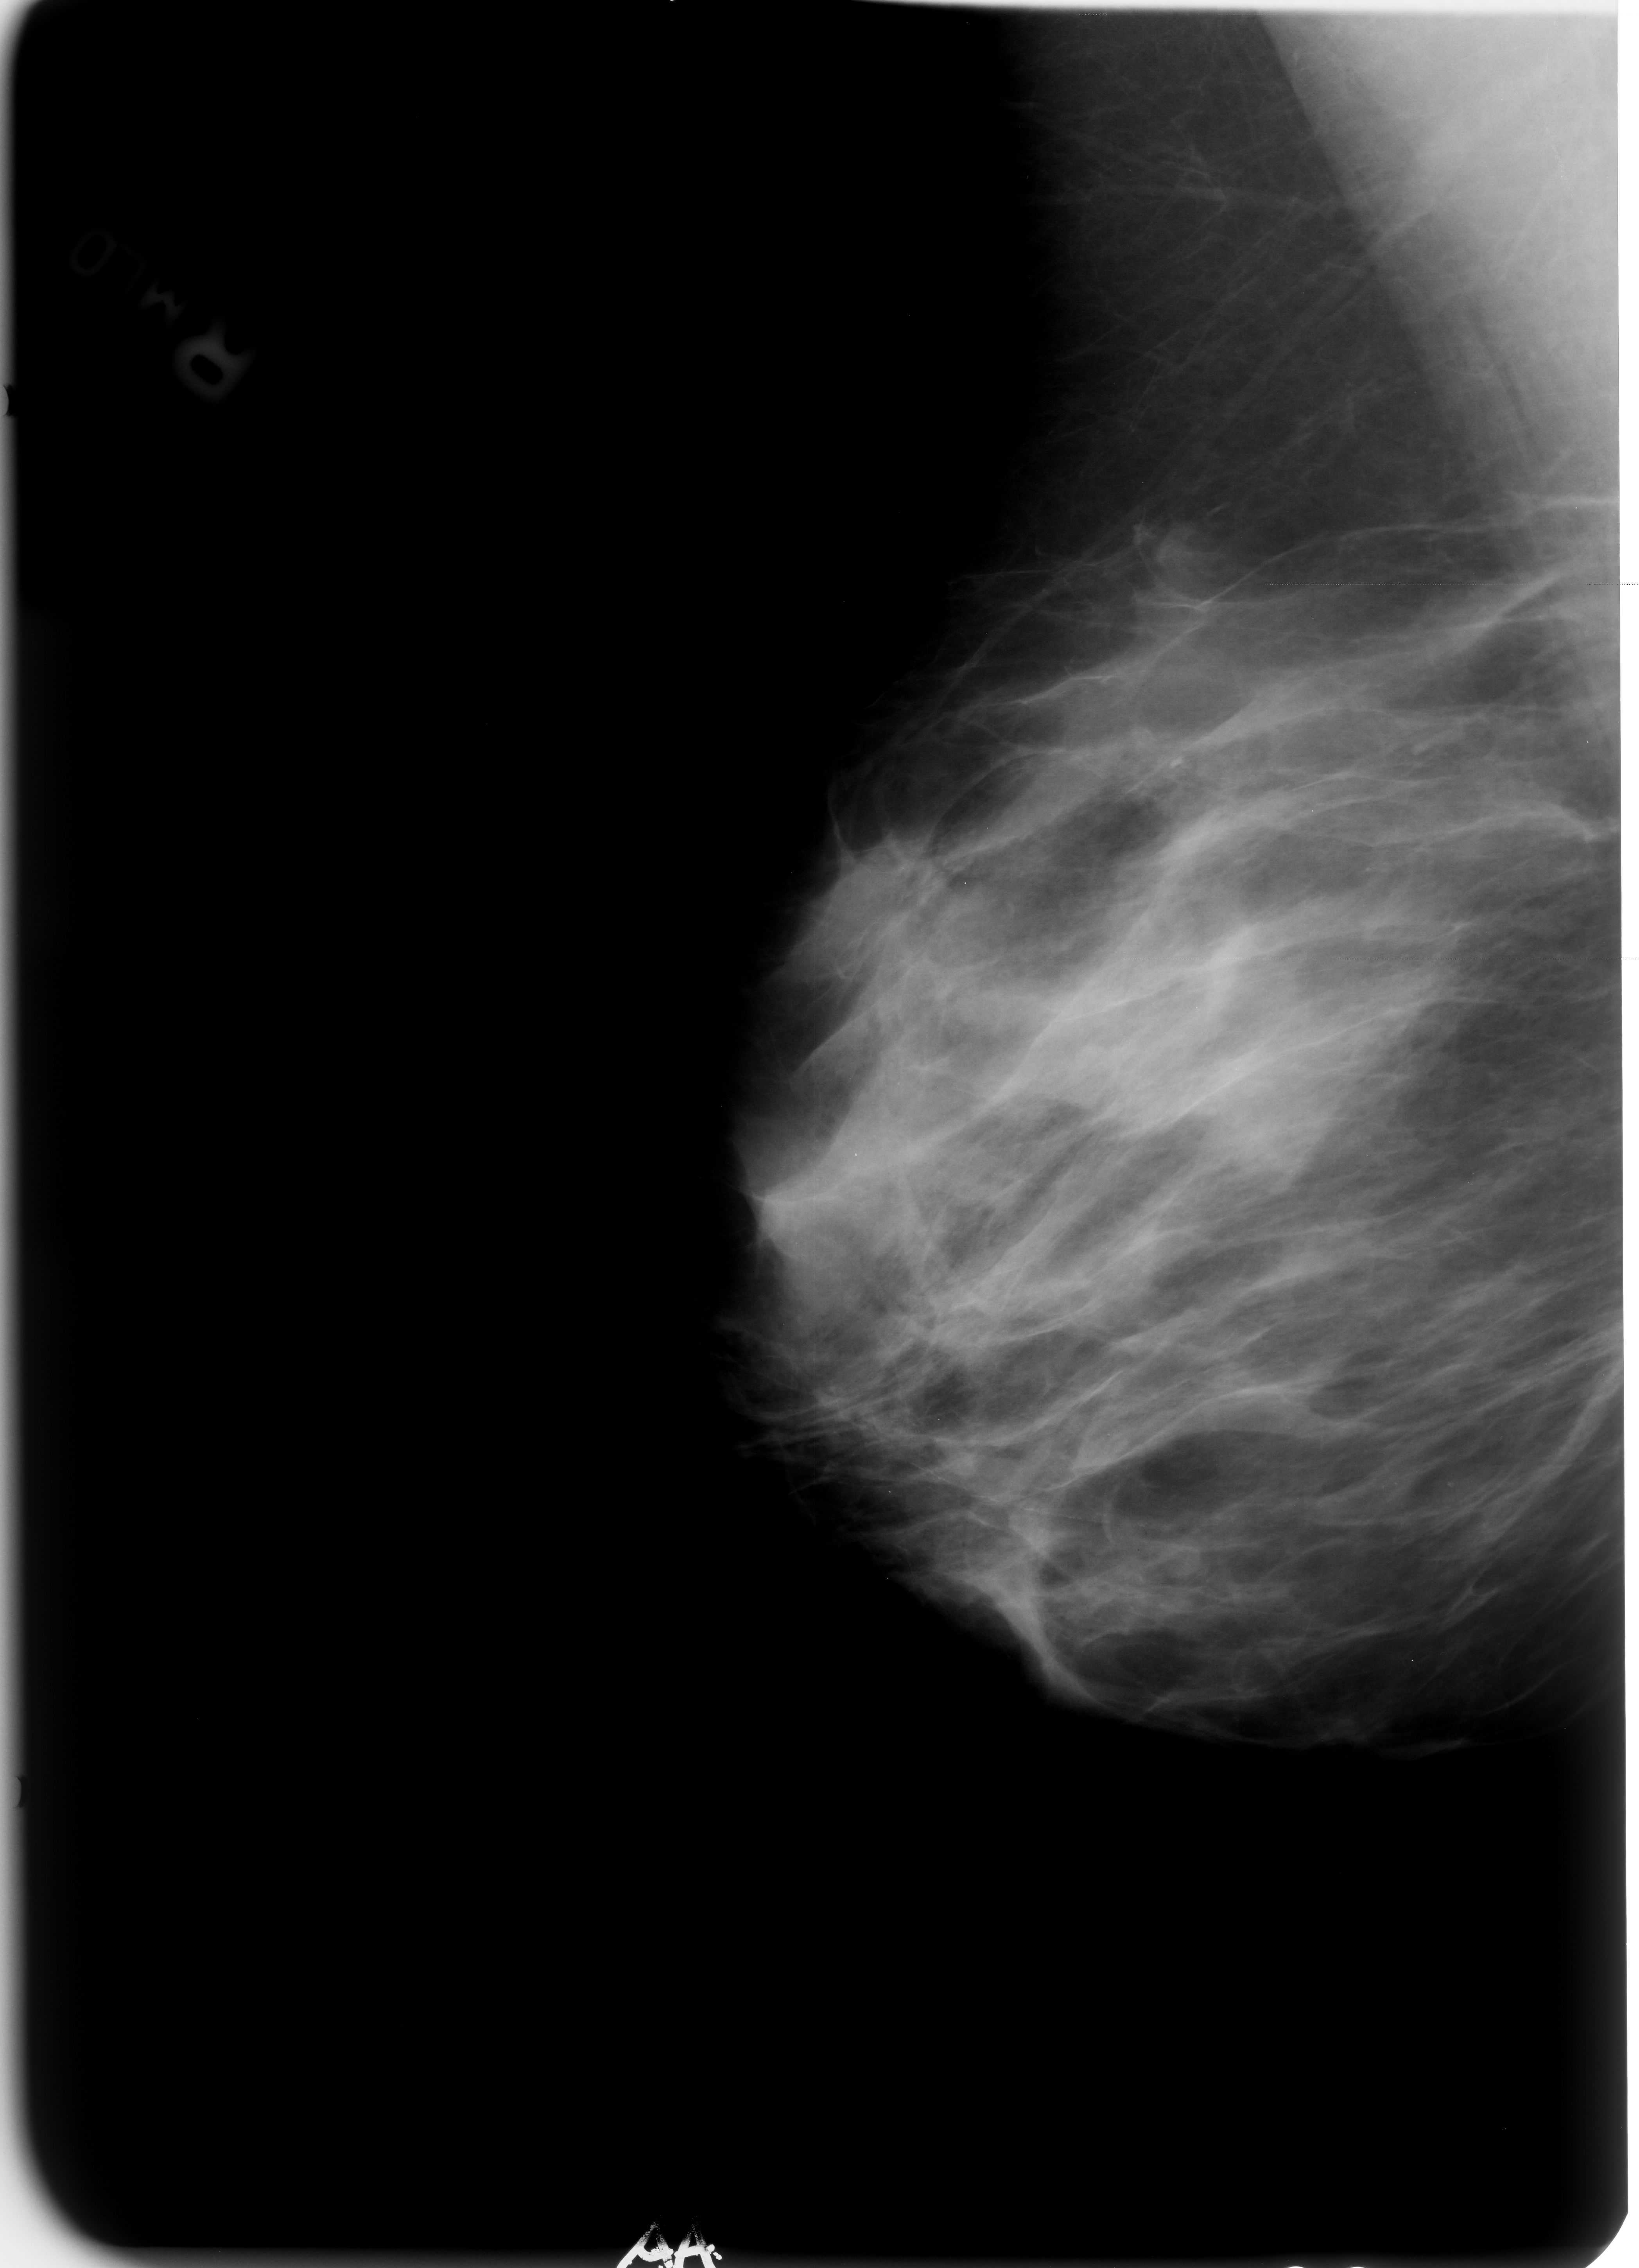
Digitized screen-film mammogram; right breast; MLO view; BI-RADS breast density category 3 (scale 1–4); 1639 × 2268 image matrix.
Expert-marked regions of interest on this image (one box per marked abnormality):
- calcifications, morphology vascular; BI-RADS assessment category 2; outcome (as recorded, no biopsy): benign without callback (not worked up further): bounding box [x1, y1, x2, y2] px = [932, 1467, 1249, 1534]